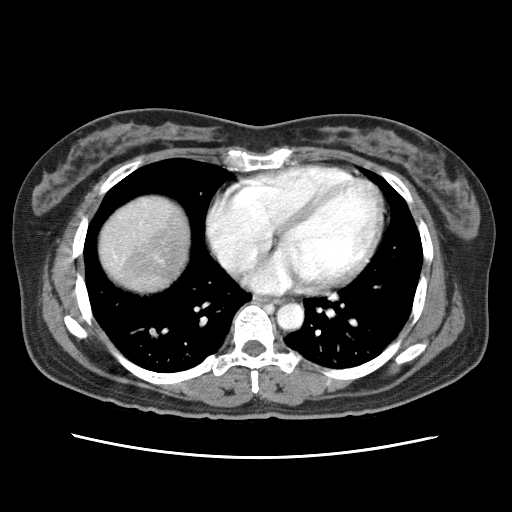
Contrast-enhanced abdominal CT (liver protocol), one axial slice; 120 kVp; soft-tissue window (W 400 / L 40 HU); 512 × 512 image matrix, field of view 340 × 340 mm. From the clinical record (not read from this slice): diagnosis: hepatocellular carcinoma (patient treated with transarterial chemoembolisation; whether this scan precedes or follows treatment is not stated here); TNM stage (as recorded): Stage-I; Child-Pugh class: A.
Structures marked on this image (semi-automatically segmented with operator editing):
- abdominal aorta: bounding box <277,302,303,330> (left, top, right, bottom; pixels)
- liver parenchyma outside the tumour (the mass and vessels are separate outlines, so this box may not span the whole liver): <100,196,188,290>